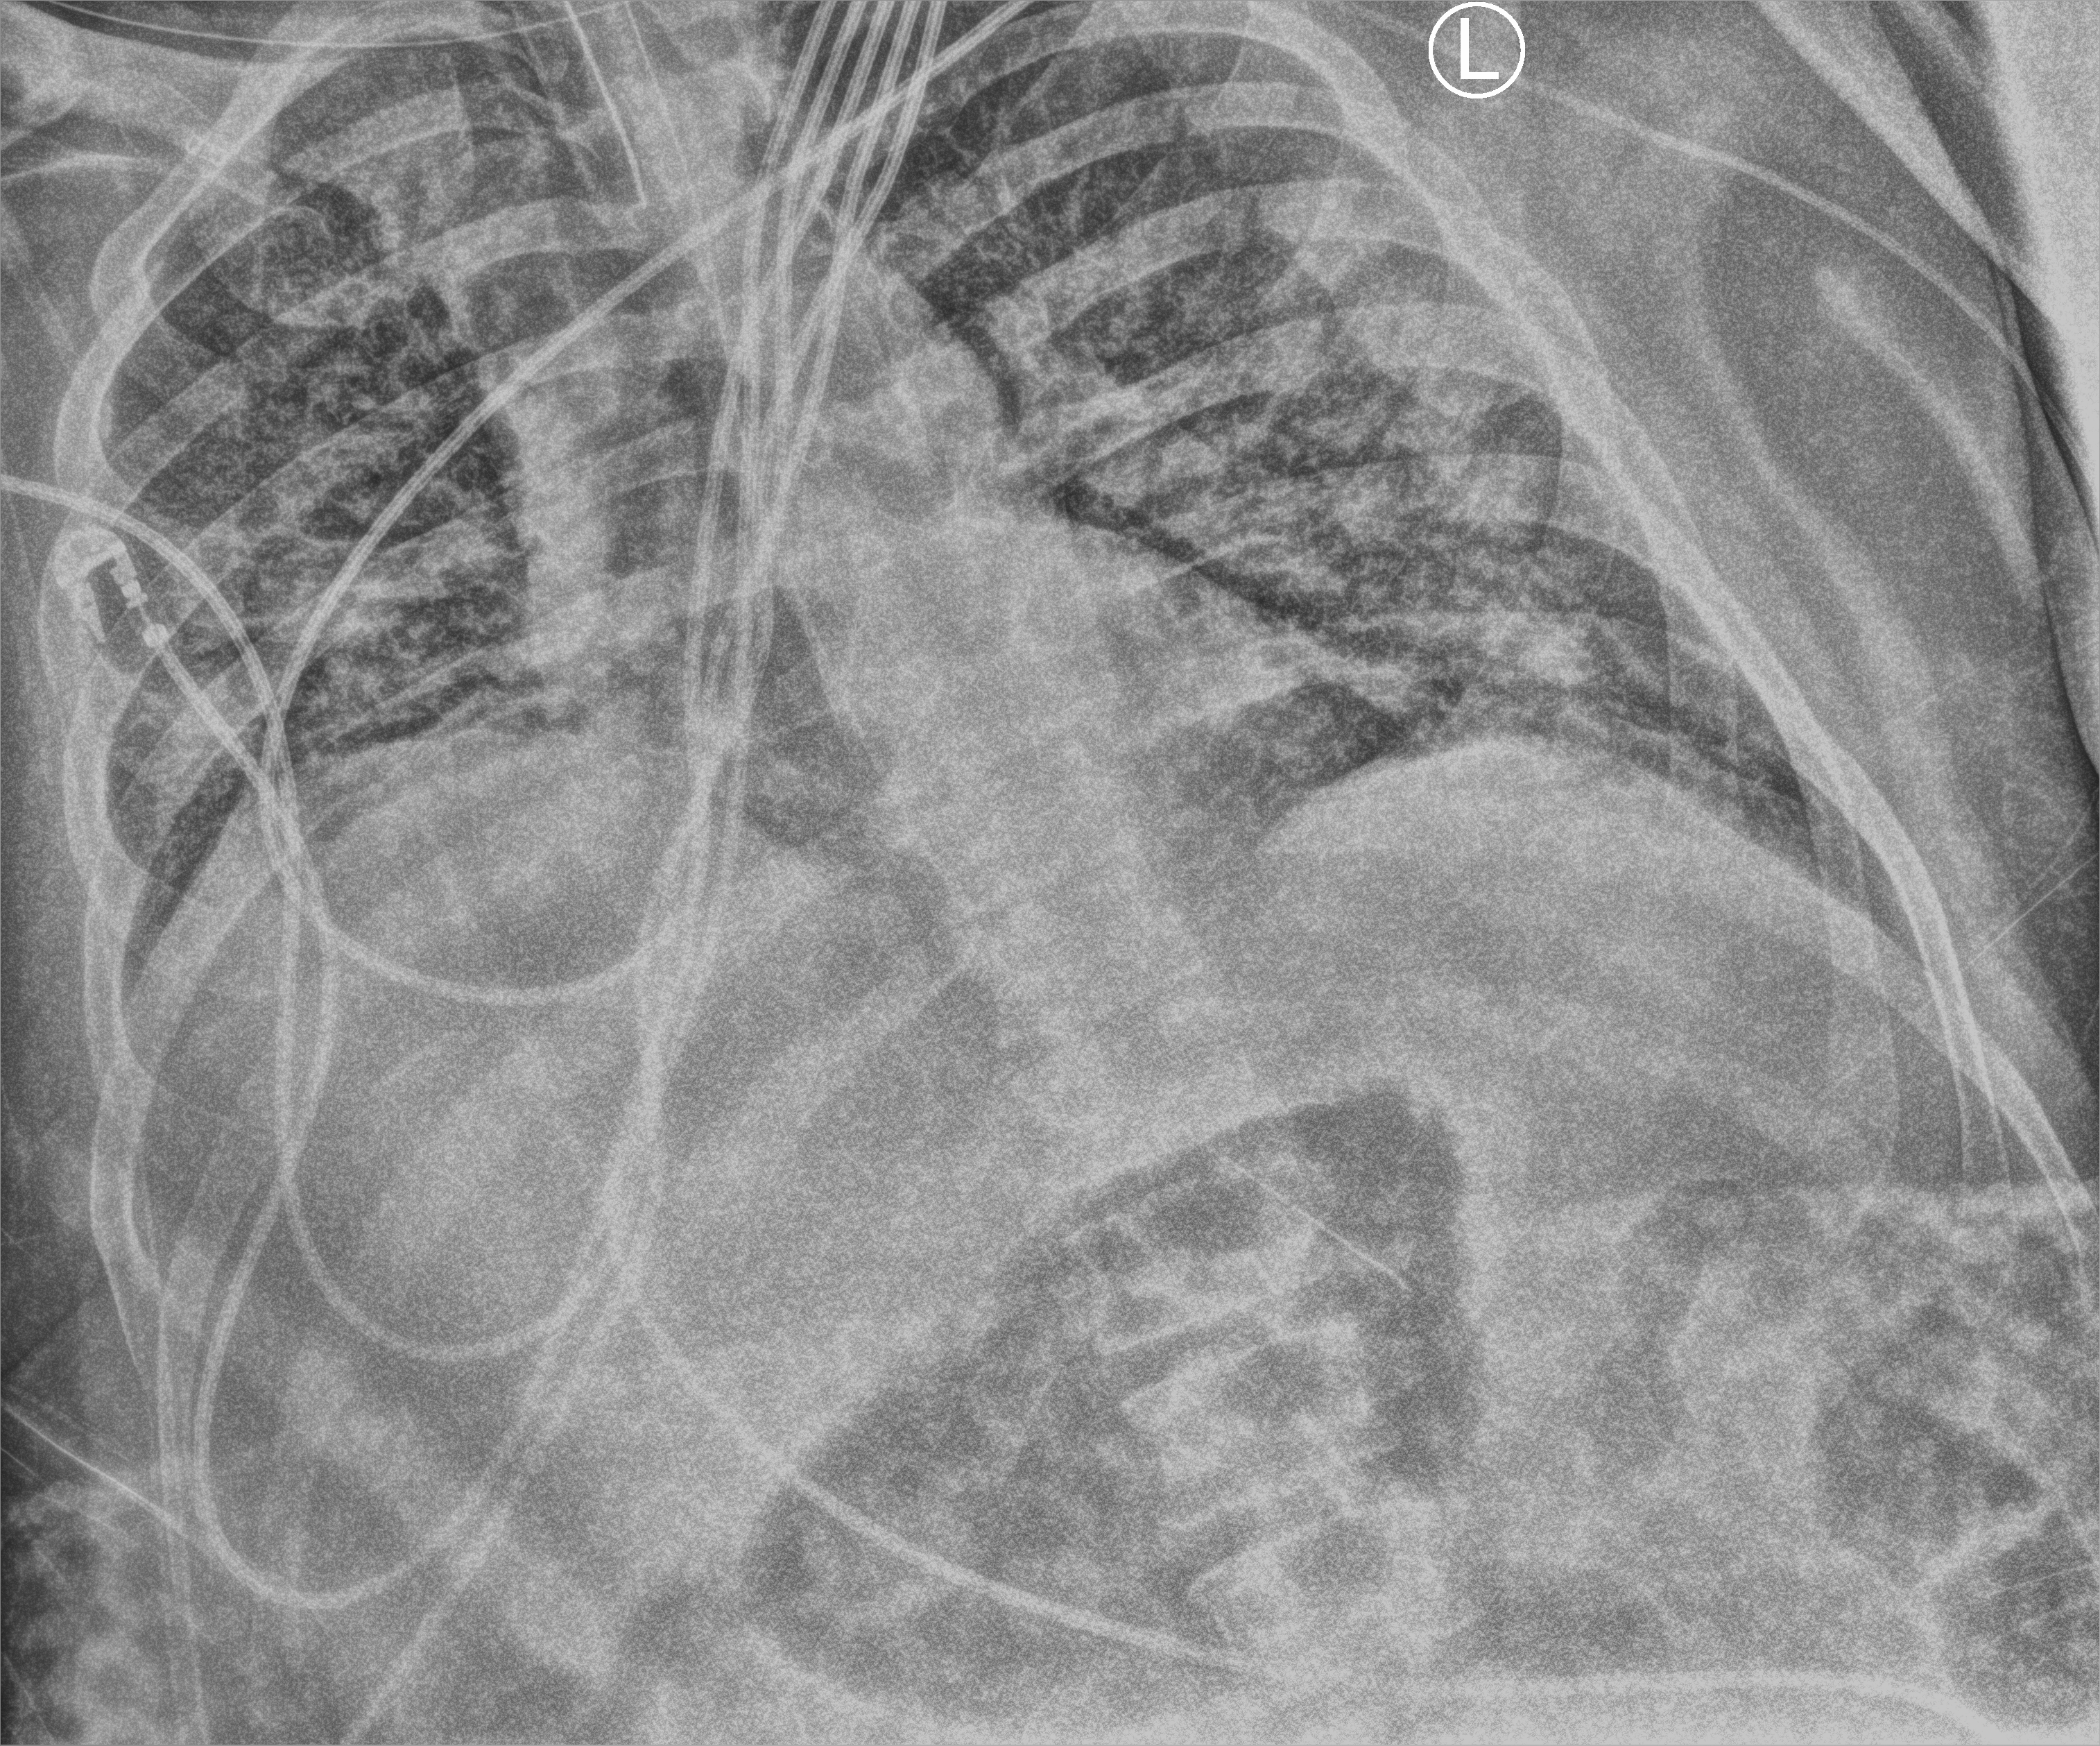
Bedside chest radiograph (computed radiography); anteroposterior (AP) projection. Male patient hospitalised with COVID-19, age 18–59 years.
Hospital-stay facts (about this admission, not read from this image; timing relative to this image not recorded): chronic kidney disease (admission record): no; length of hospital stay: 80 days.